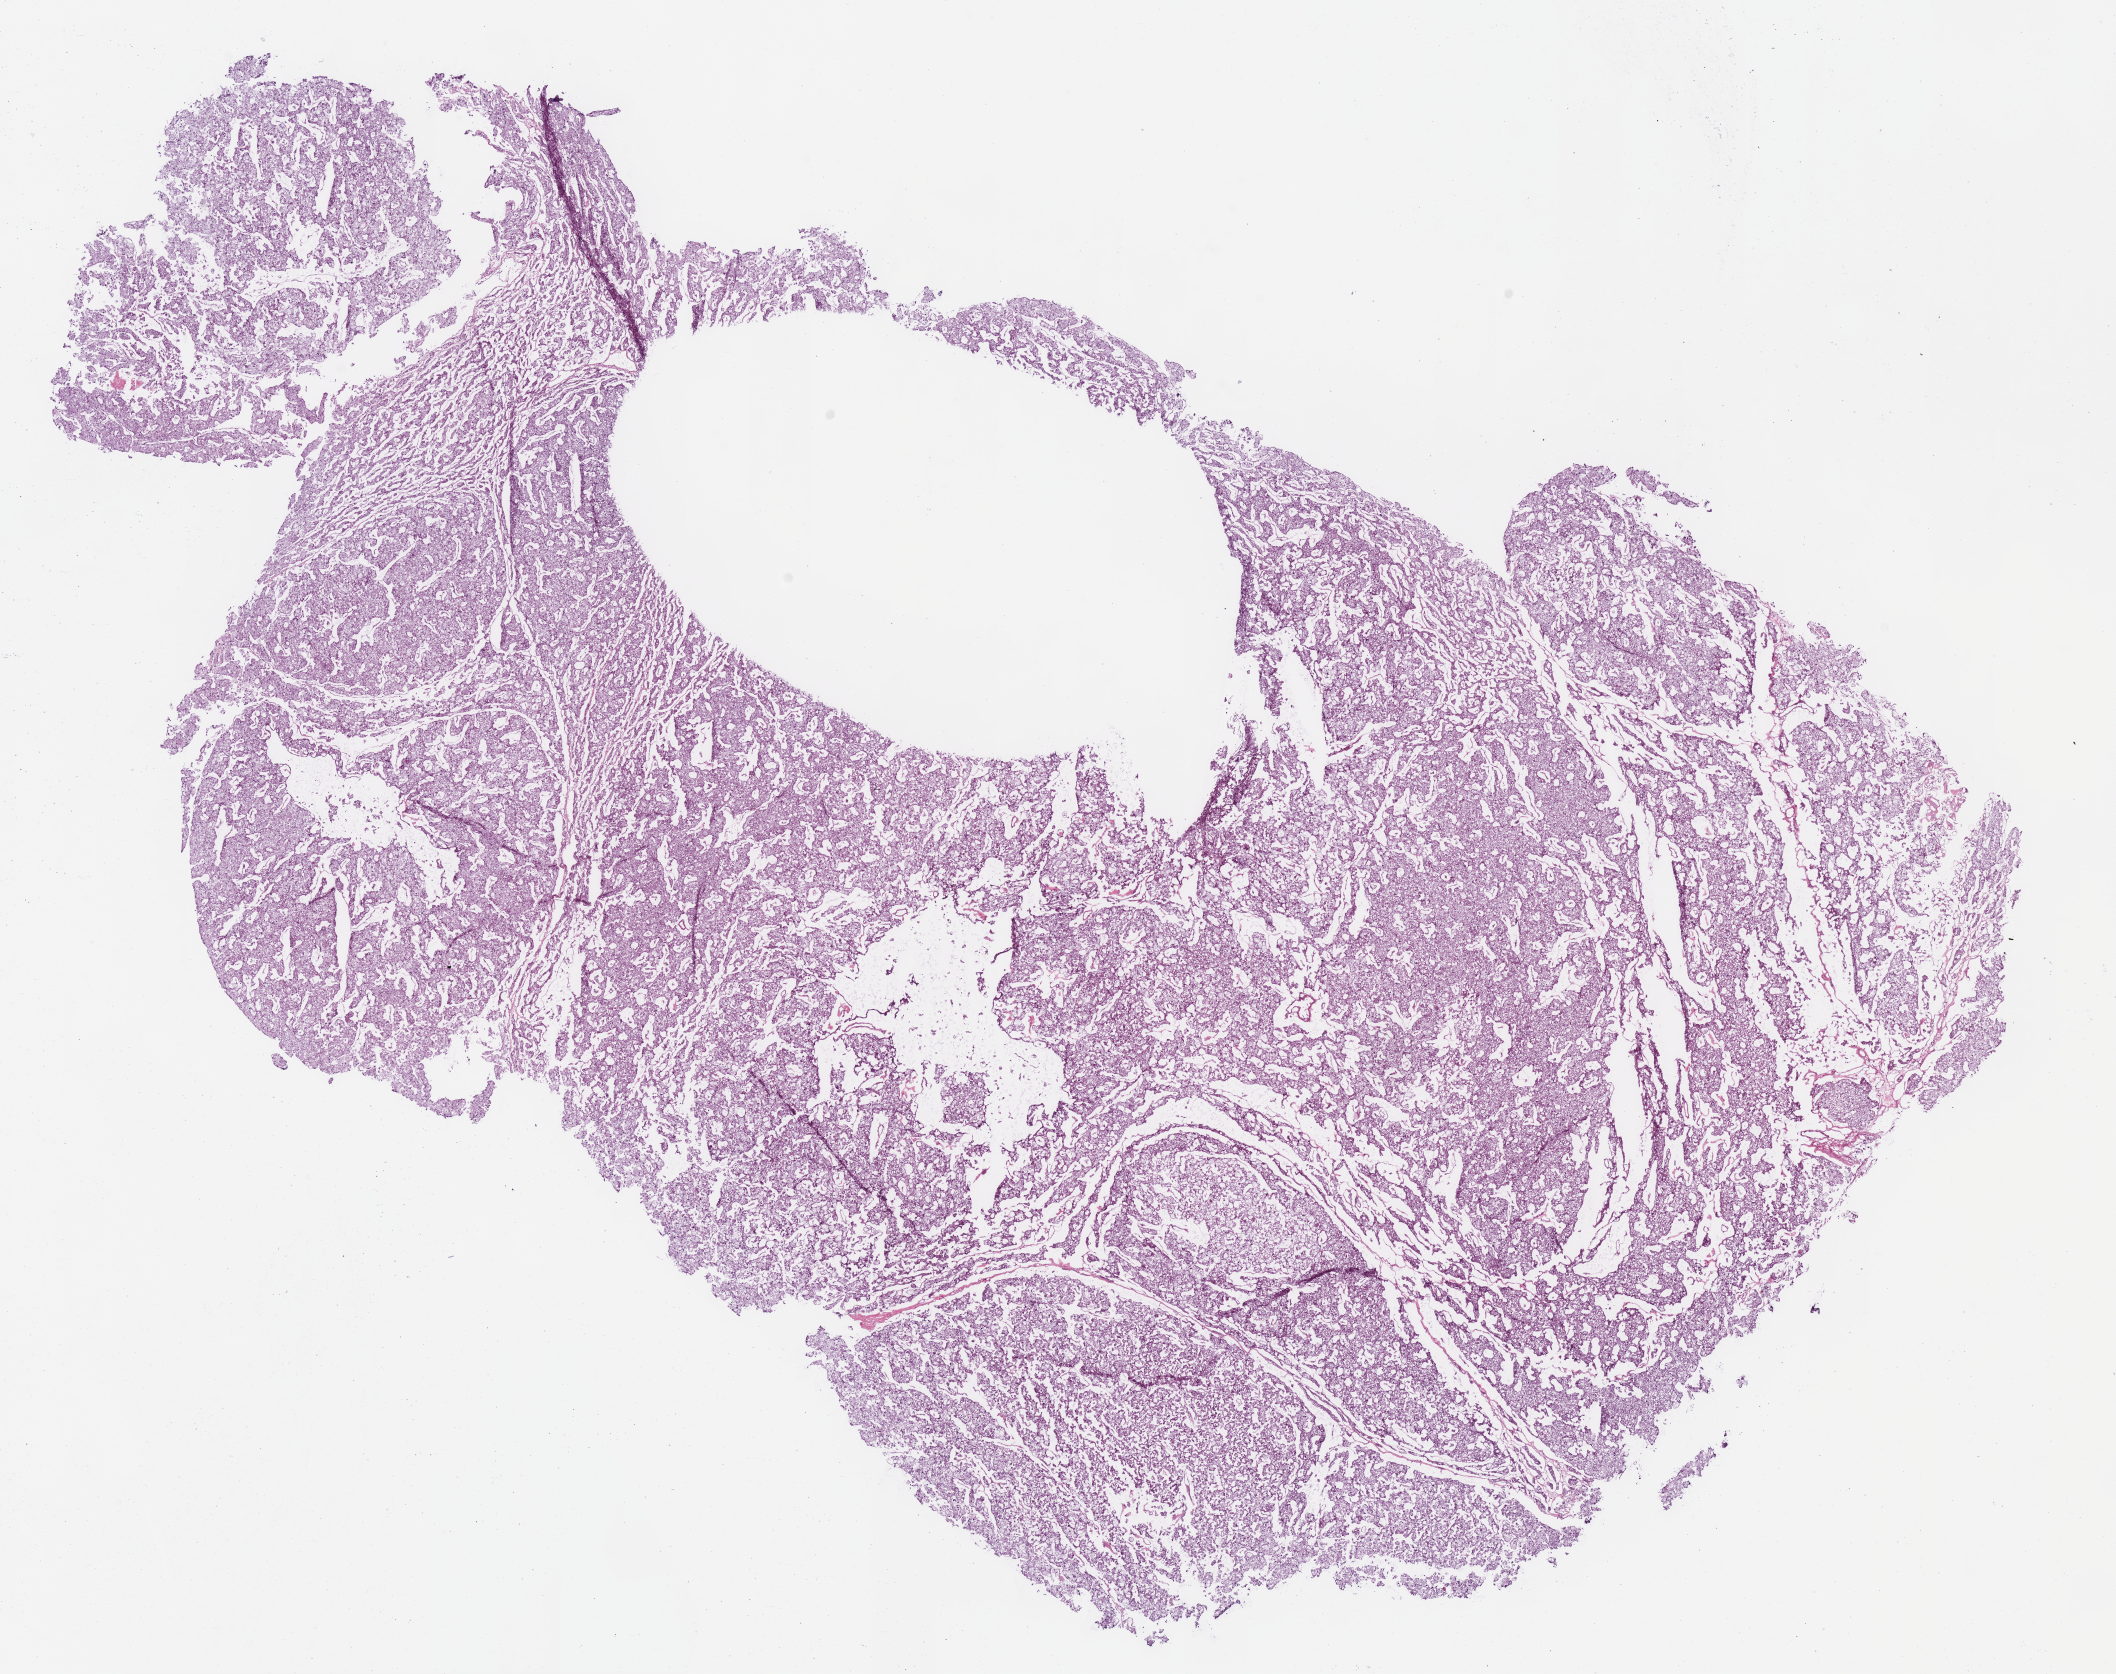
Digitized Hematoxylin and eosin (H&E) stained tissue section (whole slide) — whole scanned area (about 16.6 x 13.2 mm, acquisition: 40x scan) shown as a low-resolution overview; frozen section from the bottom of the tissue portion; primary tumour sample from the kidney. Female, age 67 years at initial diagnosis. Composition of this section per pathologist review: tumour cells 100%, tumour nuclei 90%, normal cells 0%, stromal cells 0%, necrosis 0%. Infiltration values recorded for this section: lymphocyte infiltration 1%, monocyte infiltration 0%, neutrophil infiltration 0%.
Histologic diagnosis: Renal cell carcinoma, chromophobe type. Laterality: right. AJCC pathologic stage: II.